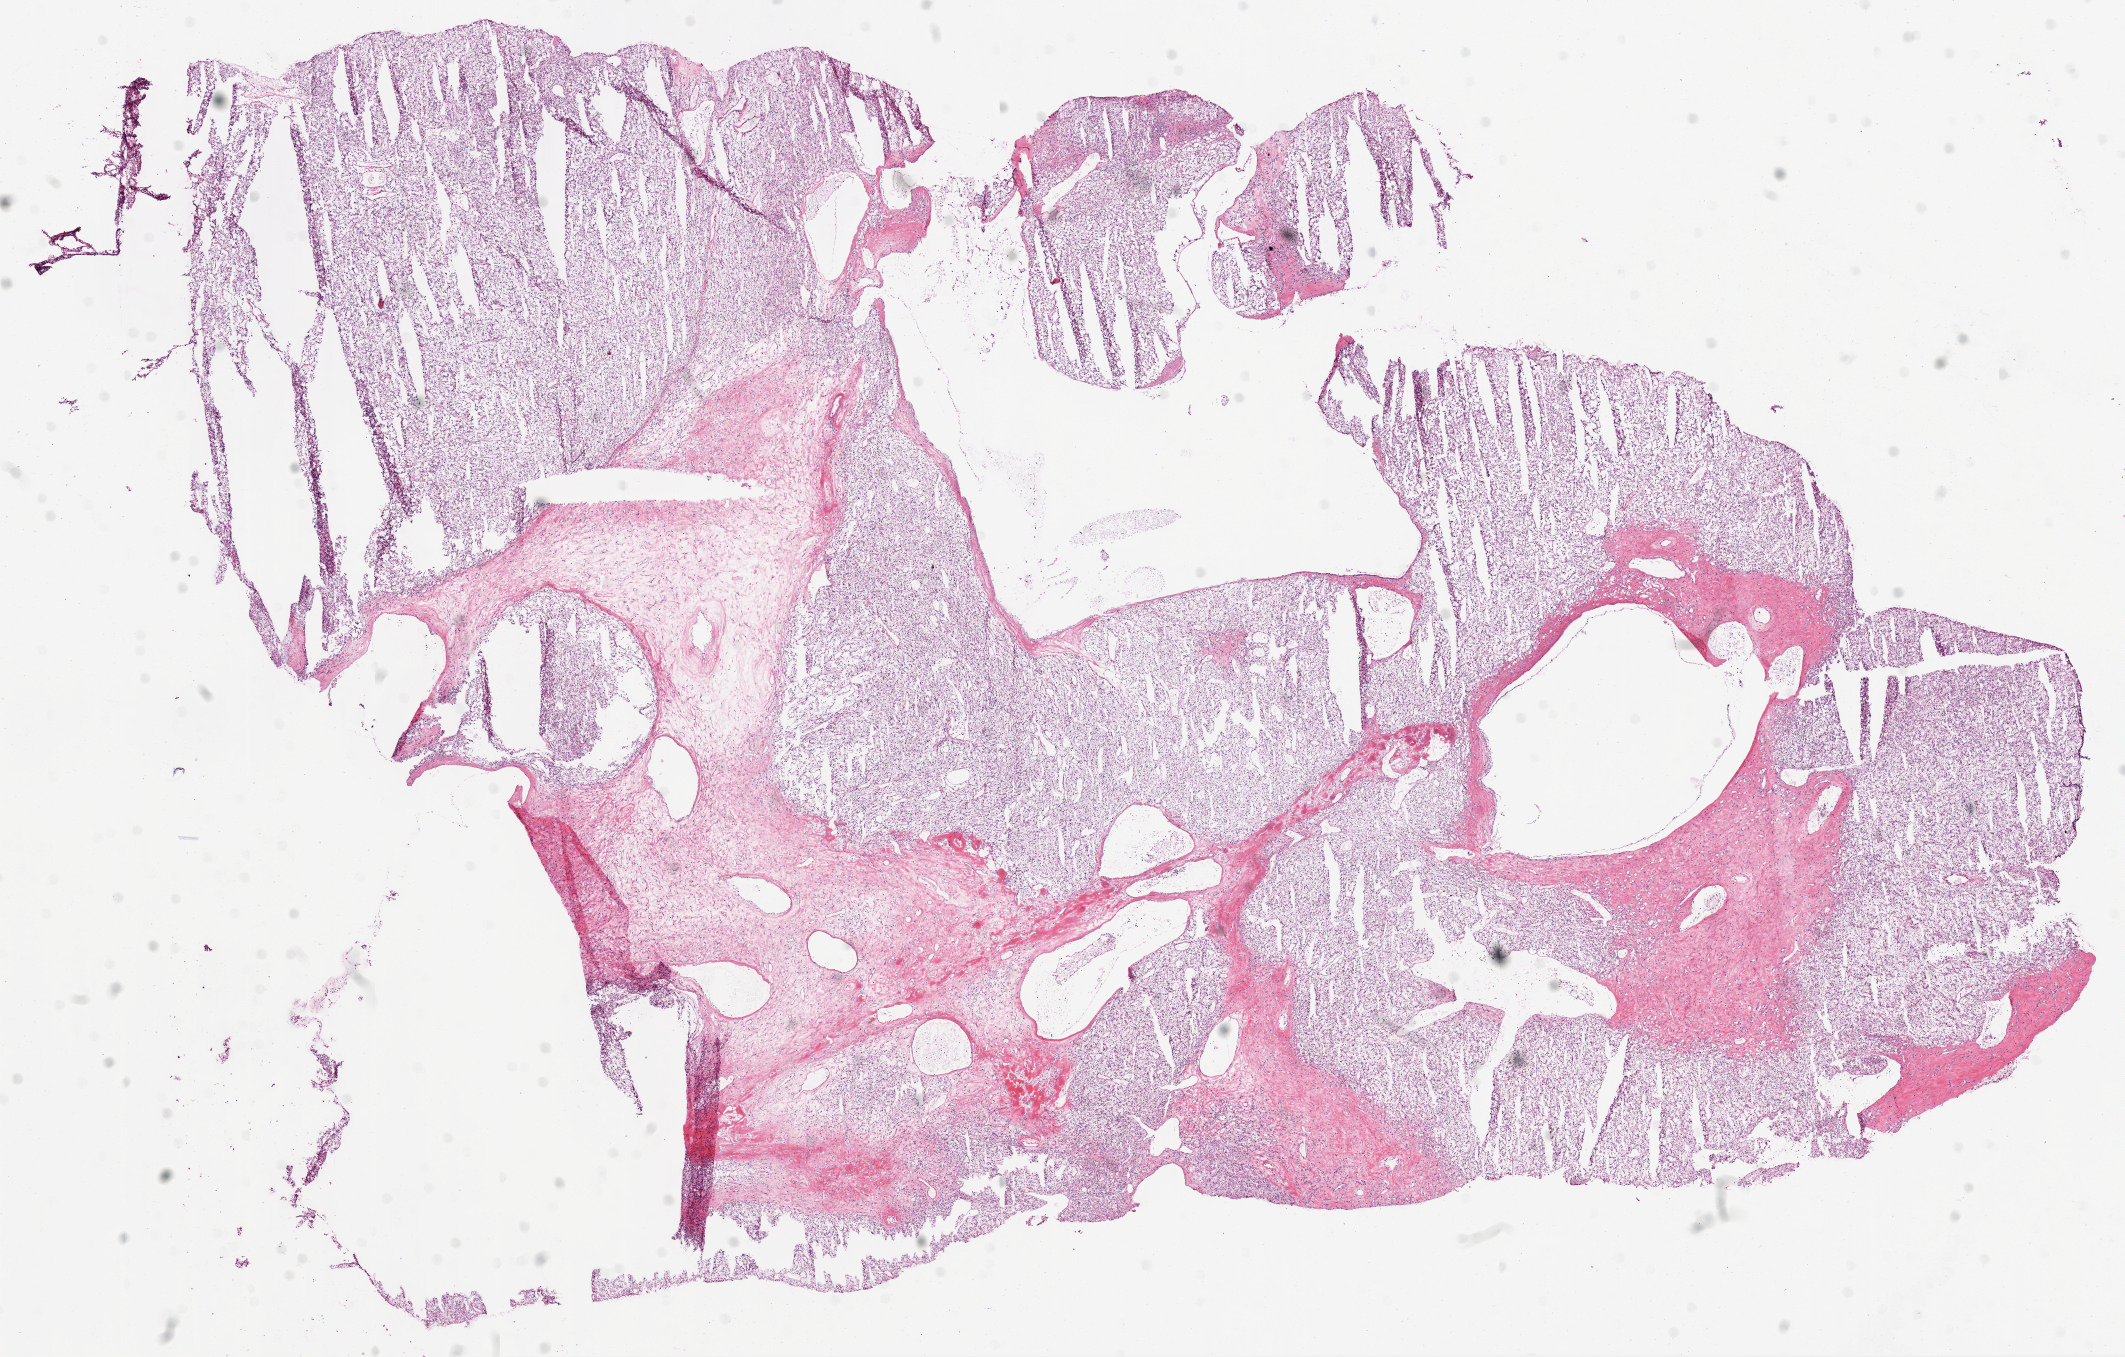
Digitized H&E tissue section (whole slide), a low-resolution overview of the entire scanned area, about 17.1 x 10.9 mm (acquisition: 20x scan), frozen section from the bottom of the tissue portion, sample: primary tumour, kidney. Patient: female, age at initial diagnosis 72 years. Histologic grade: G2 (moderately differentiated). Slide review estimates, as recorded: tumour cells 70%, tumour nuclei 90%, normal cells 0%, stromal cells 30%, necrosis 0%.
Diagnosis: Clear cell adenocarcinoma, NOS. AJCC pathologic stage: I.